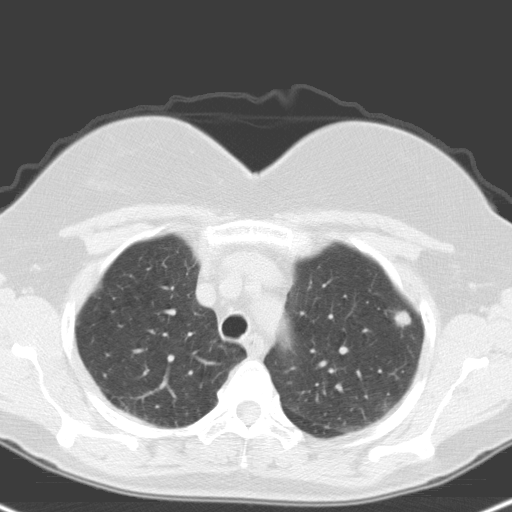
Low-dose screening chest CT, axial slice; first (baseline) screen; lung window (W 1500 / L -600 HU); 512 × 512 image matrix. Female, age 59 years at enrolment. Current smoker at enrolment.
Expert reader's lesion annotation, bounding box <383,295,425,340> (left, top, right, bottom; pixels). The screening reader recorded 2 non-calcified nodules or masses ≥4 mm on this exam (right upper lobe, left upper lobe); which of them this box marks is not recorded. Official screen result: positive, change unspecified: nodule(s) >= 4 mm or enlarging nodule(s), mass(es), or other non-specific abnormalities suspicious for lung cancer. Participant outcome: lung cancer diagnosed 48 days after this screen — large cell neuroendocrine carcinoma, left upper lobe, poorly differentiated (G3), stage IA (AJCC 6th edition), 12 mm at pathology.